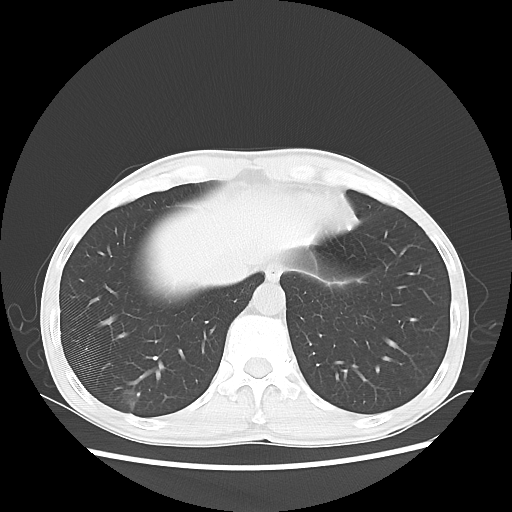
Chest CT, one axial slice; slice 16 of 68 in the series (ordered by position); reconstruction kernel LUNG; lung window (W 1500 / L -600 HU); 5 mm slice thickness; 512 × 512 image matrix, field of view 360 × 360 mm. Patient: male, 60 years. From the clinical record (not read from this slice): clinical TNM (as recorded): T1c N0 M0.
Annotated regions visible in this slice (rectangle marked by the reading radiologist):
- lung tumour (recorded histology: adenocarcinoma): bounding box (x1, y1, x2, y2) in pixels: (117, 385, 148, 419)